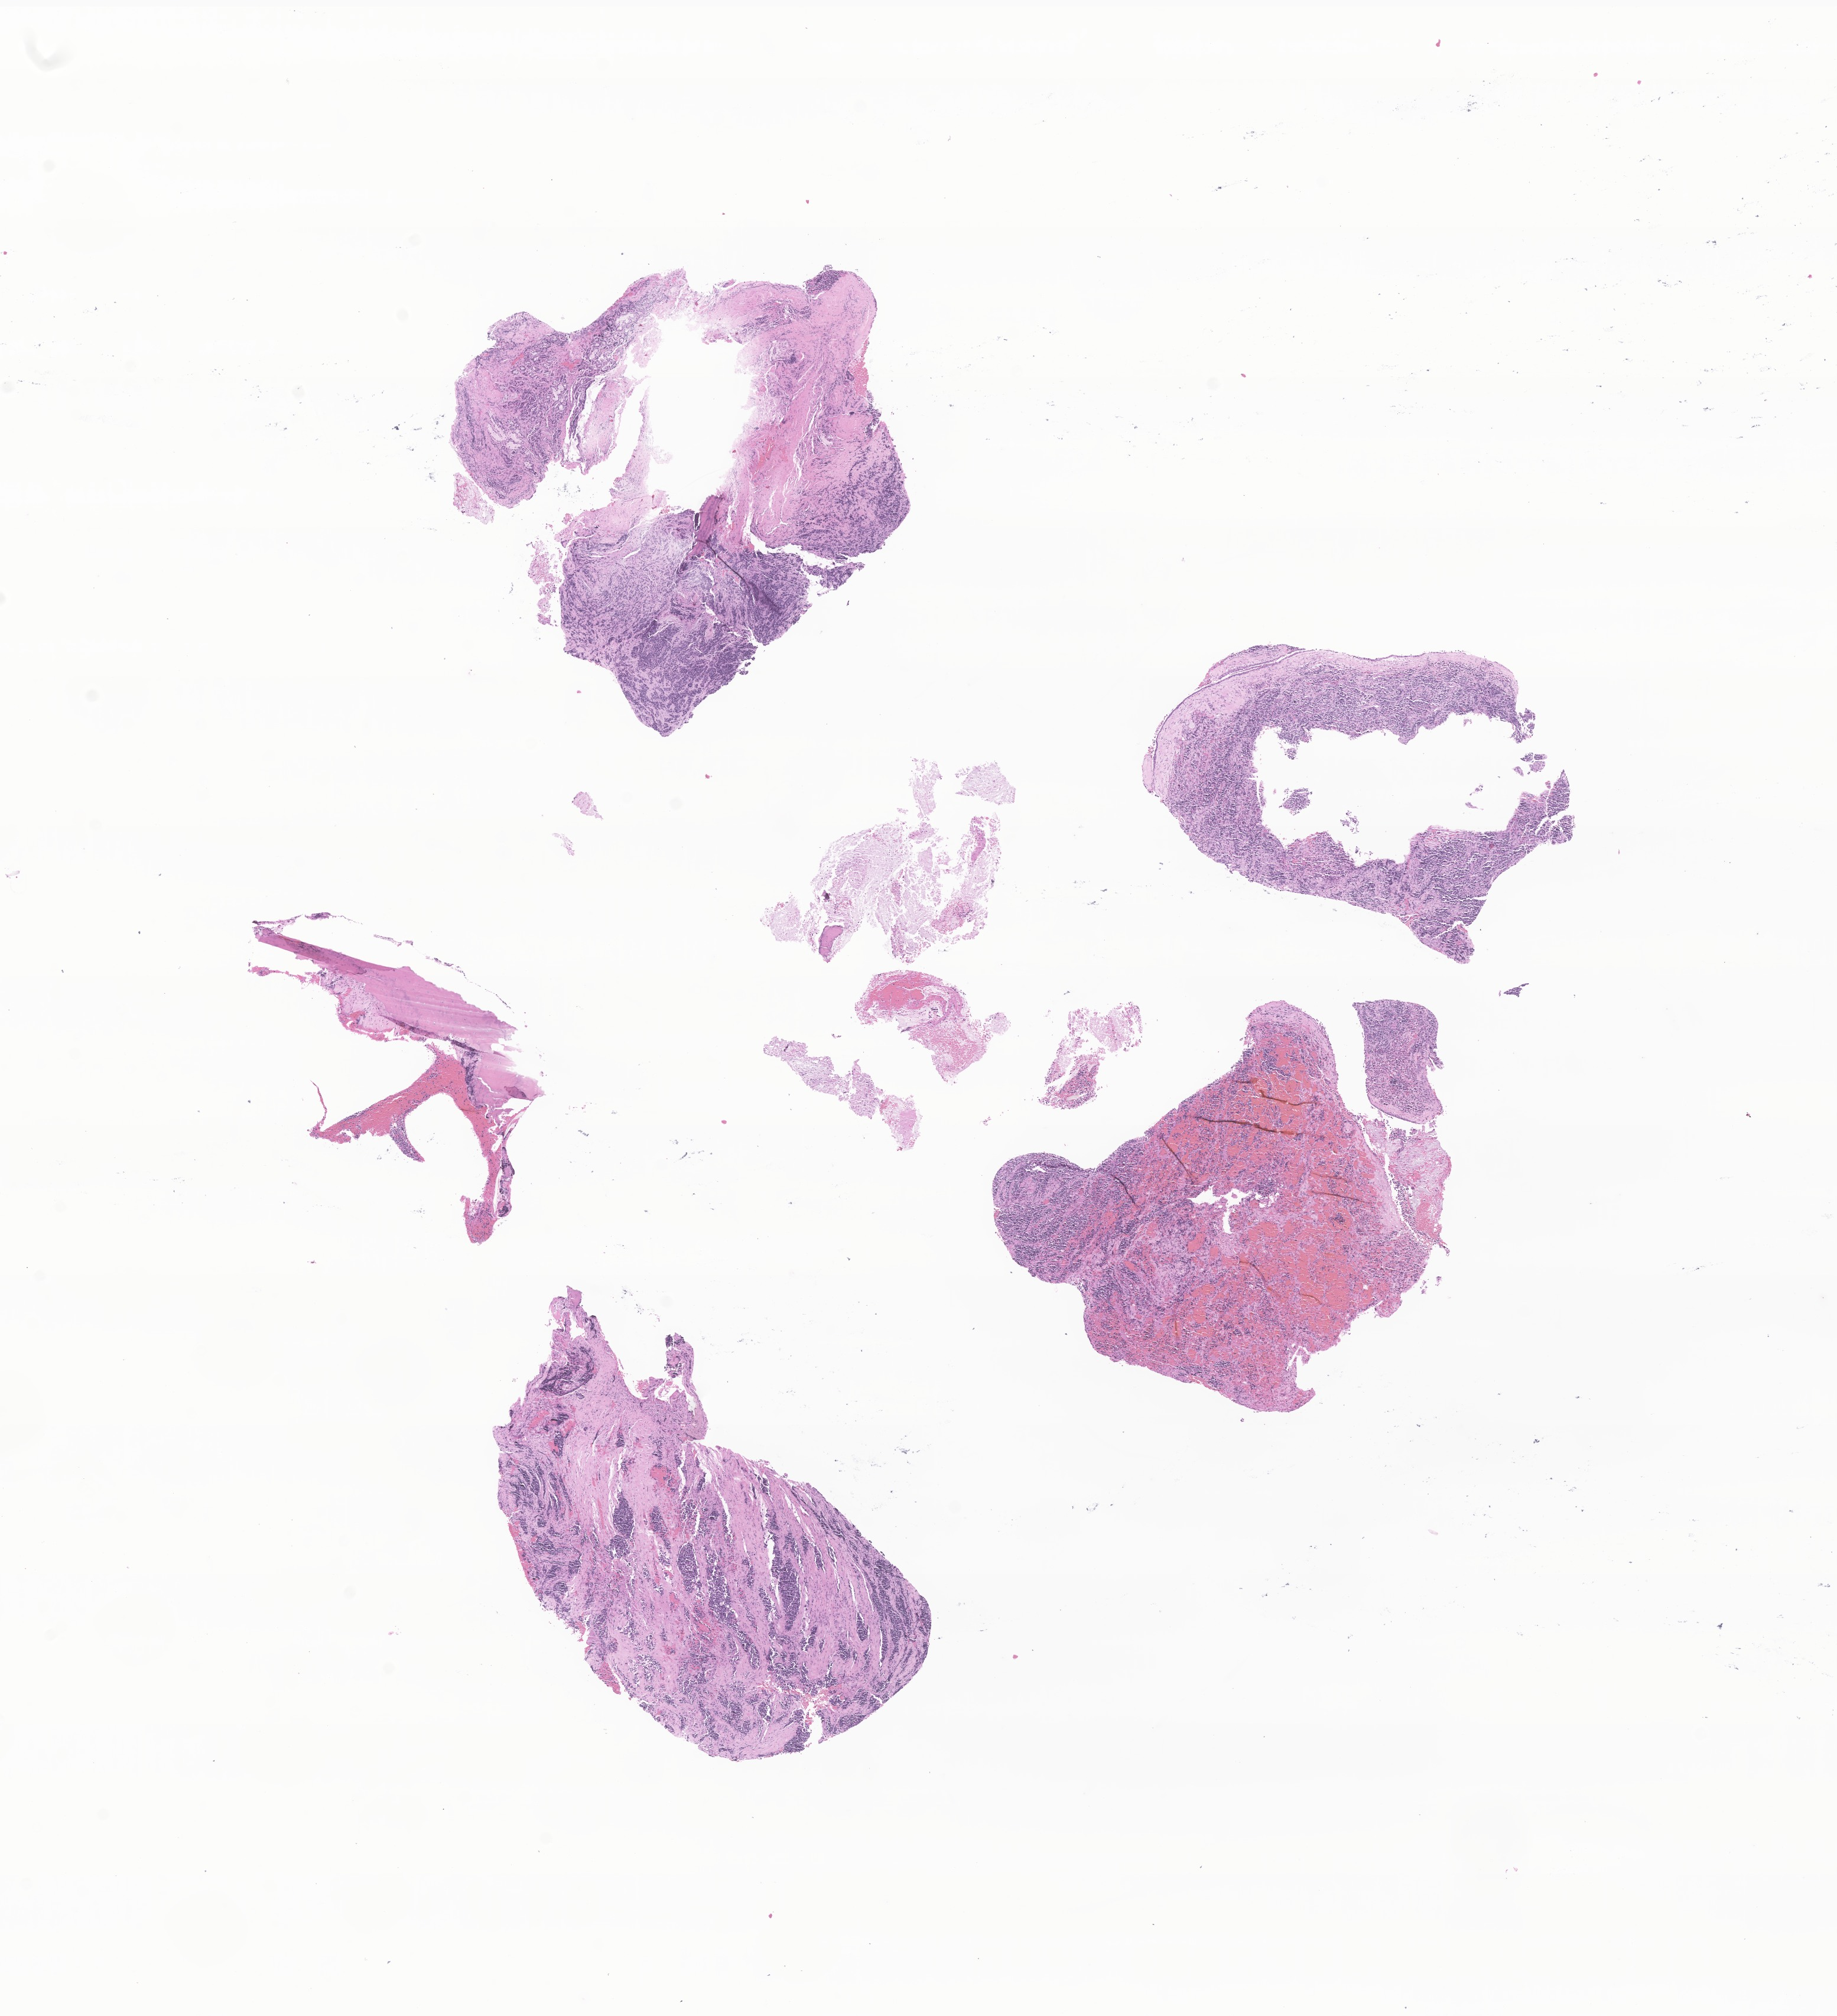
Whole-slide image, haematoxylin and eosin stain of tumor tissue from the soft tissues of head and neck — low-resolution overview of the scanned area, about 13.1 x 14.4 mm; formalin-fixed paraffin-embedded section. Patient: male, age 191 months (15 years 11 months).
• recorded diagnosis: Rhabdomyosarcoma, NOS